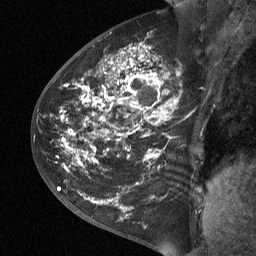
Breast MRI (dynamic contrast-enhanced), one sagittal slice. Position 31 of 64 along the scan axis. Dynamic contrast-enhanced study with each time point stored as its own series, time point 2 of 3 at this slice position (early post-contrast, ordered by acquisition time). 1.5 T. TE 4.8 ms, TR 27 ms. 256 × 256 image matrix, field of view 200 × 200 mm. Female patient, age 42 years. Case-level facts recorded for this patient, not image findings: setting: breast cancer imaged before/during neoadjuvant chemotherapy; receptor status: triple-negative.
Outlined on this slice (semi-automatic segmentation, software-assisted and operator-edited):
- analysis volume of interest (the breast-tissue region the enhancement analysis was run in; not a lesion): box from (x=43, y=29) to (x=202, y=190) px
- tumour enhancement mask (voxels above the 90 % enhancement threshold inside the analysis volume of interest): (x=66, y=48)–(x=169, y=163)